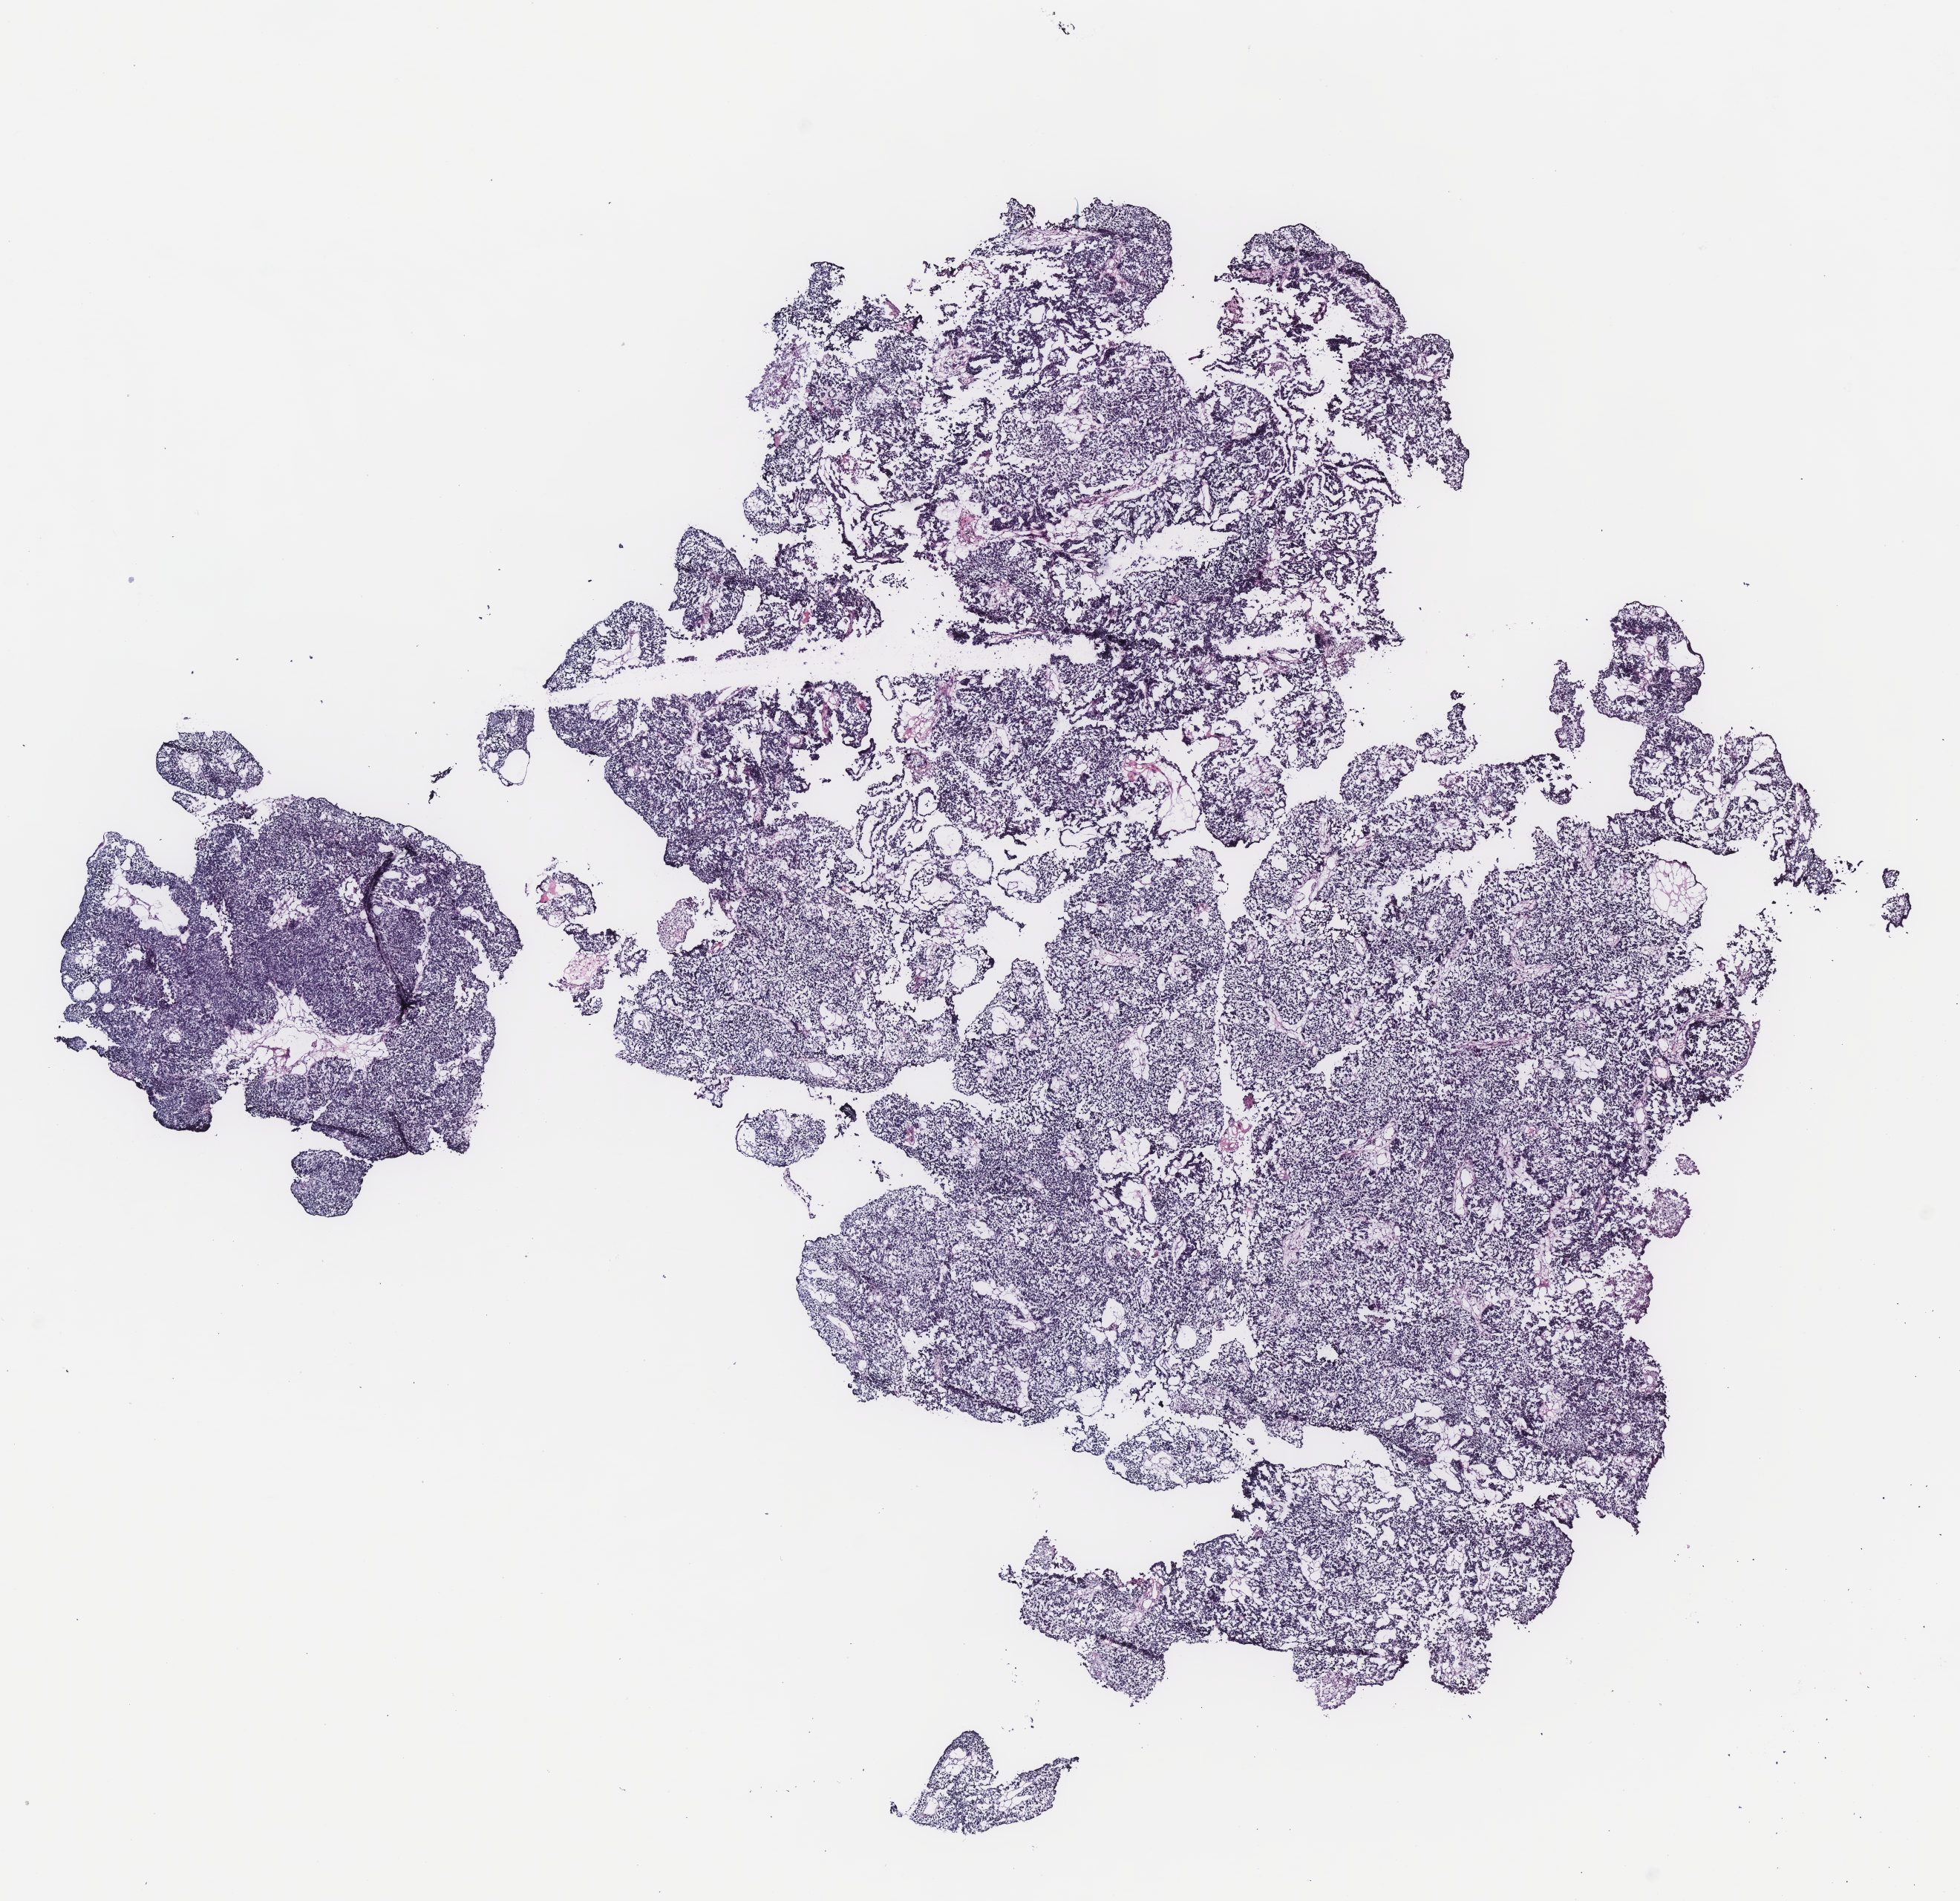
Digitized H&E tissue section (whole slide), a low-resolution overview of the entire scanned area, about 10.6 x 10.2 mm (slide scanned at 40x); ovary, tissue type not recorded.
Patient diagnosis (cohort enrolment): ovarian cancer (ovary).